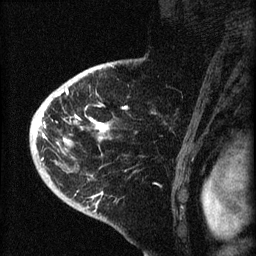
Breast MRI (dynamic contrast-enhanced), one sagittal slice; slice 50 of 60 in the series (ordered by position); dynamic contrast-enhanced series, image 2 of 4 at this slice position (ordered by acquisition); 1.5 T; TE 4.2 ms, TR 8.2 ms; 2 mm slice thickness; 256 × 256 image matrix. Female patient, age 71 years.
Annotated regions visible in this slice (semi-automatically segmented with operator editing):
- analysis volume of interest (the breast-tissue region the enhancement analysis was run in; not a lesion): bounding box <35,75,153,190> (left, top, right, bottom; pixels)
- tumour enhancement mask (voxels above the 70 % enhancement threshold inside the analysis volume of interest): <36,88,125,161>